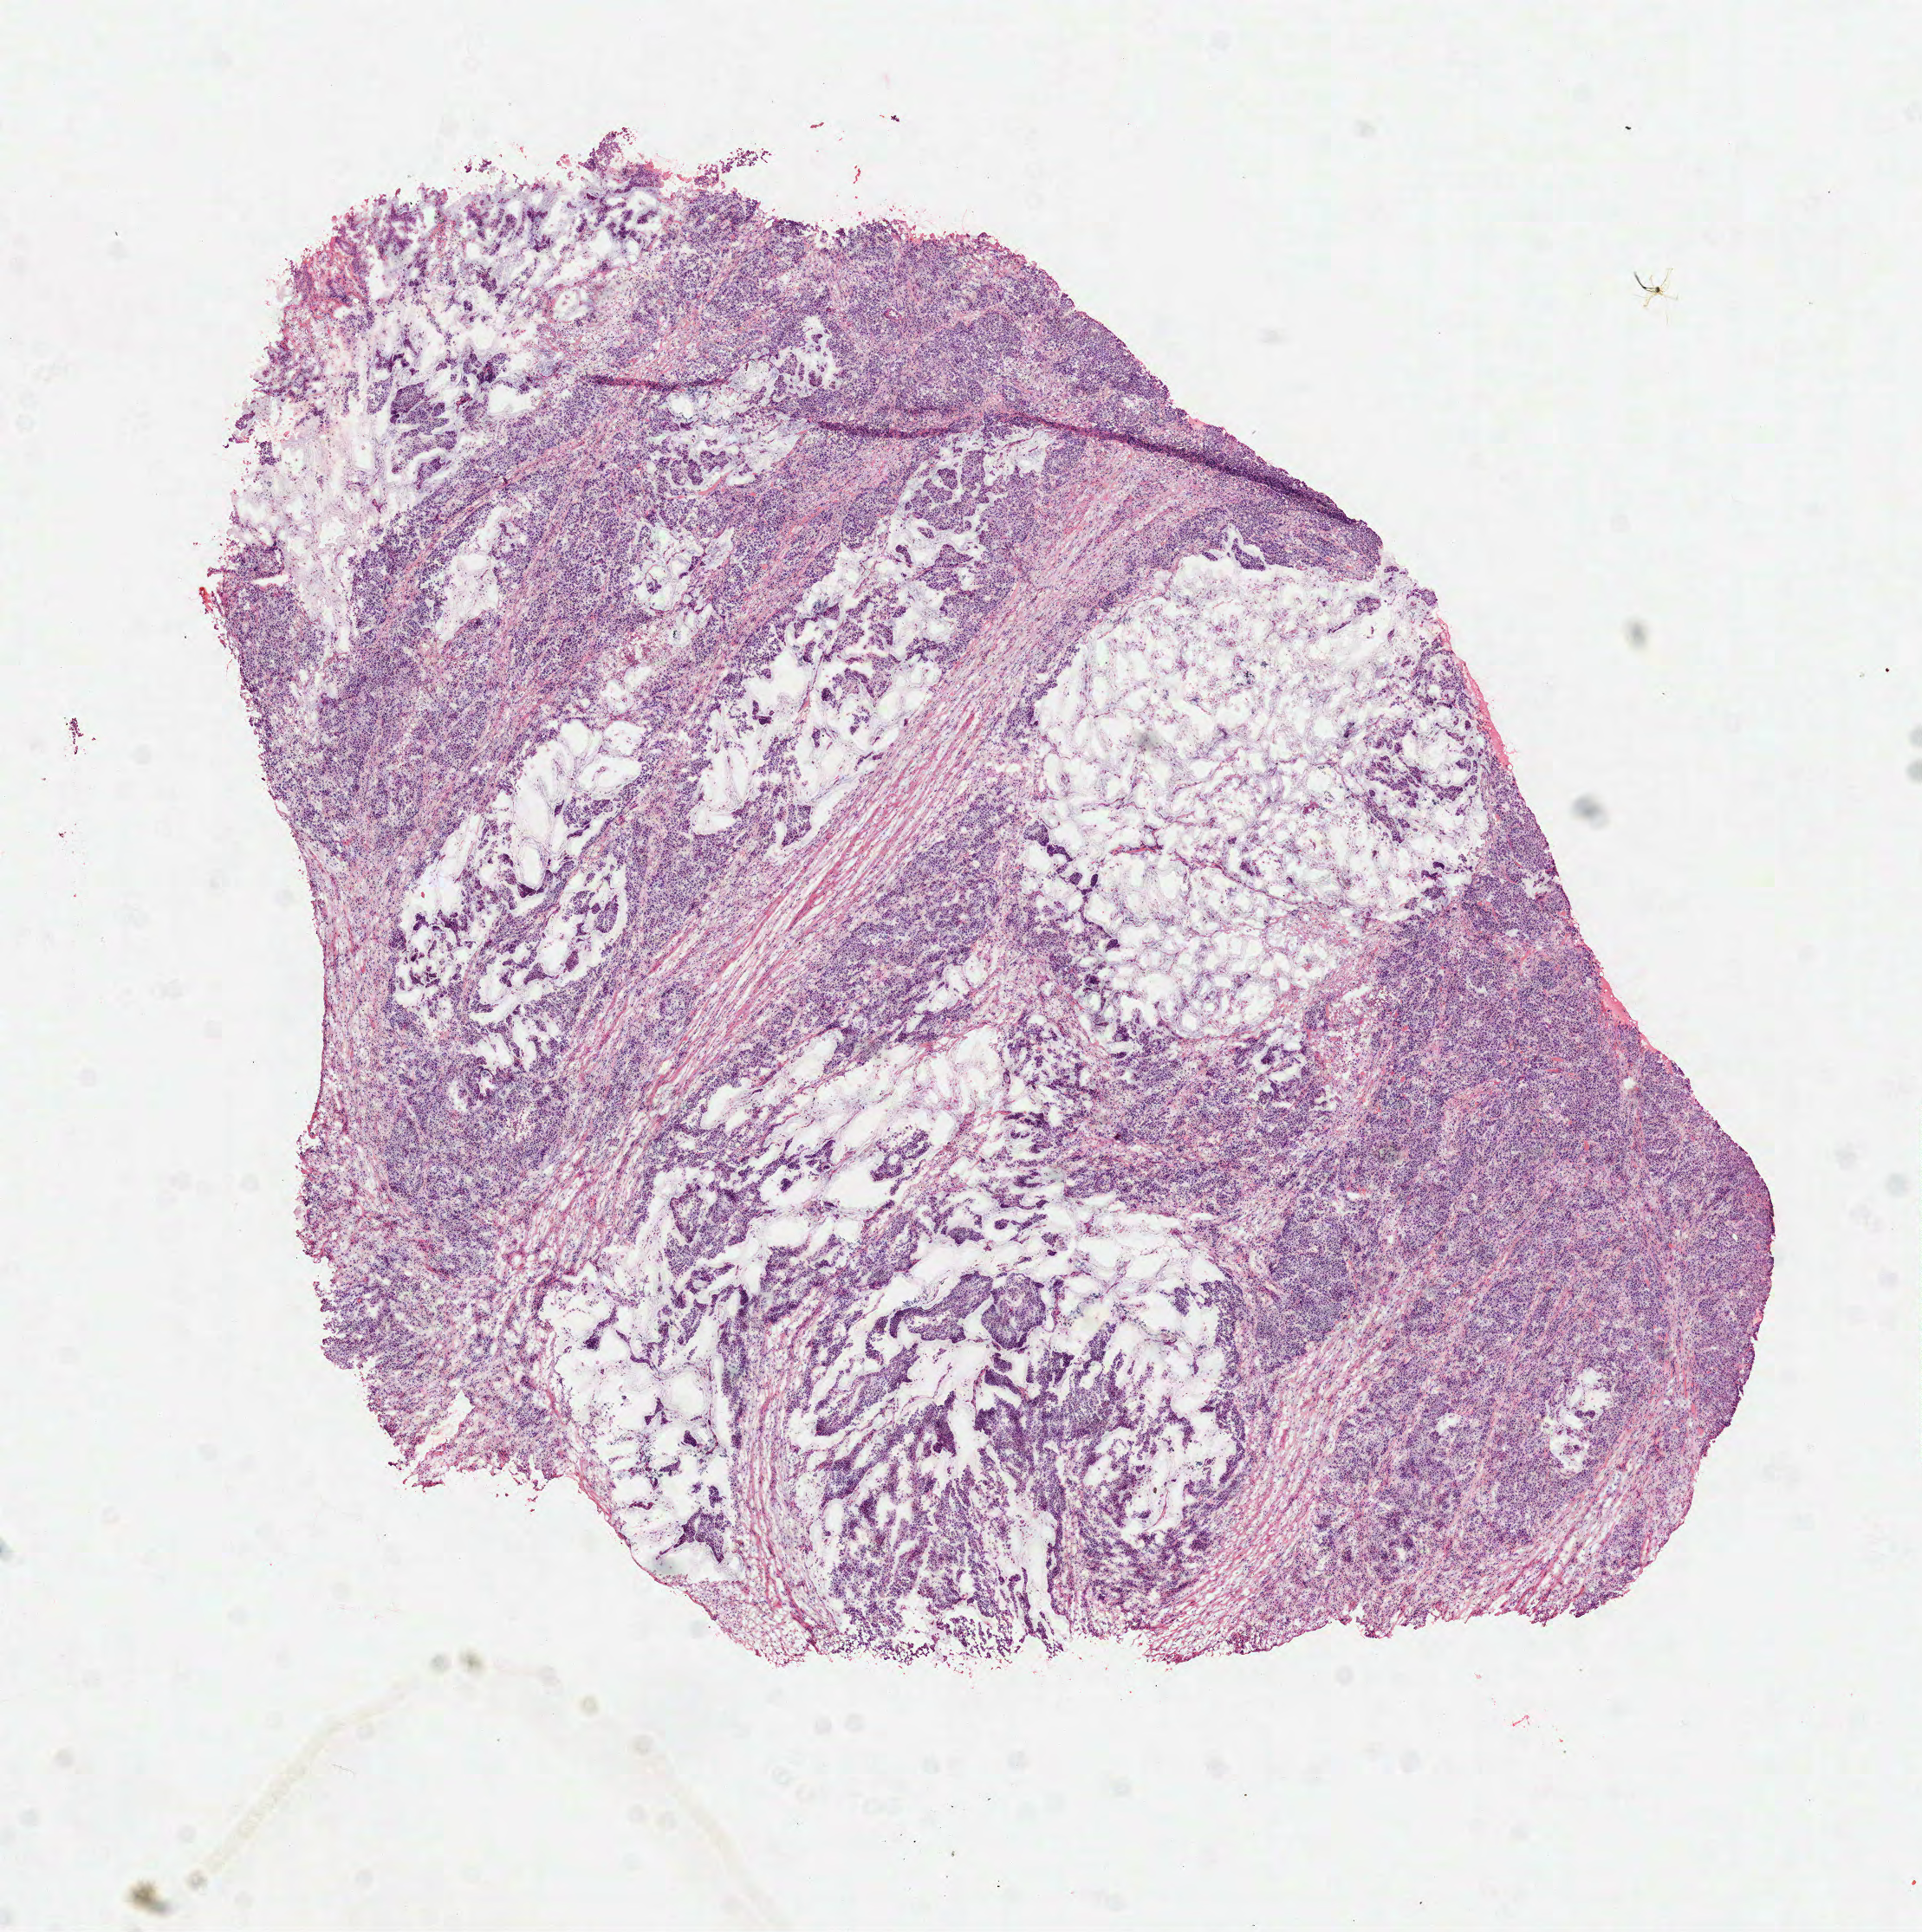
Whole-slide histology image, H&E-stained, low-resolution overview of the scanned area, about 8.9 x 9.0 mm (from a 40x scan); frozen section from the top of the tissue portion; sample: primary tumour, colon. Female, age 71 years at initial diagnosis. Composition of this section per pathologist review: tumour cells 90%, tumour nuclei 80%, normal cells 0%, stromal cells 10%, necrosis 0%.
Diagnosis: Adenocarcinoma, NOS (ascending colon). TNM: T1 N0 M0. AJCC pathologic stage: I (6th edition).